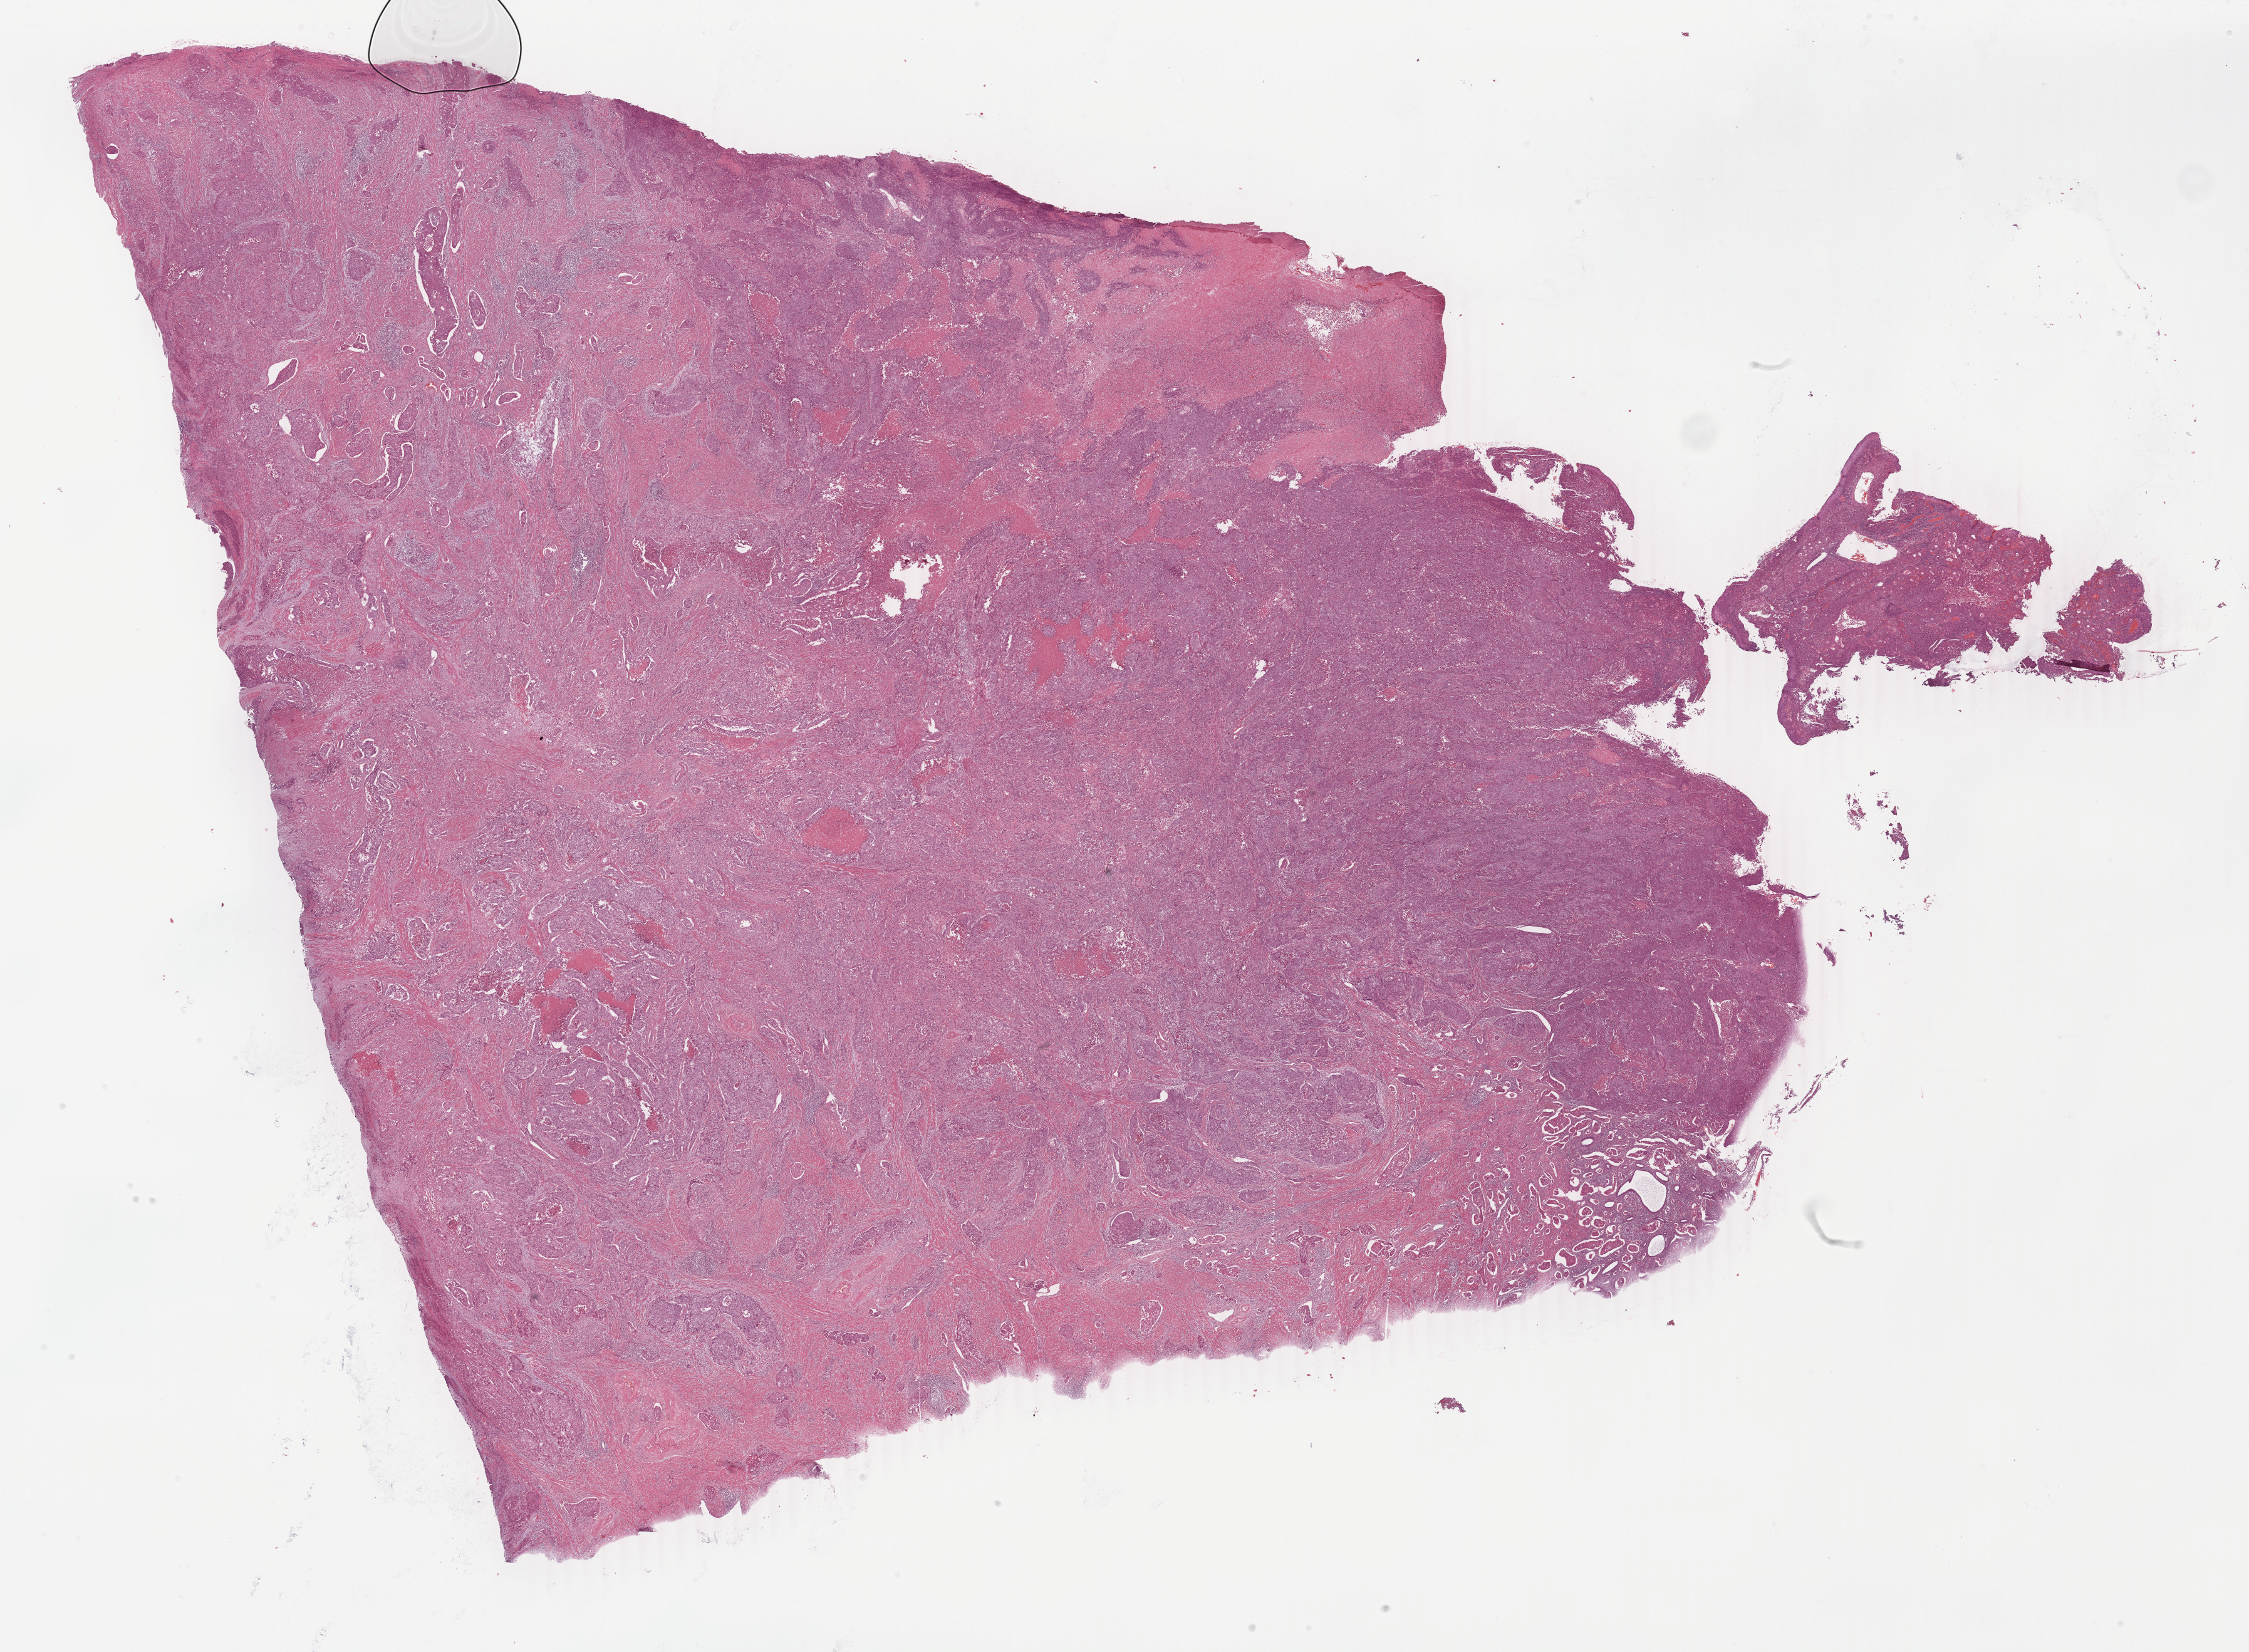
H&E-stained whole-slide image, whole scanned area (about 28.6 x 21.0 mm) shown as a low-resolution overview; FFPE section; sample: primary tumour, uterus. Female, age 35 years at initial diagnosis. Histologic grade: G3 (poorly differentiated).
FIGO stage: IVB. Pathologic diagnosis: Endometrioid adenocarcinoma, NOS (corpus uteri).